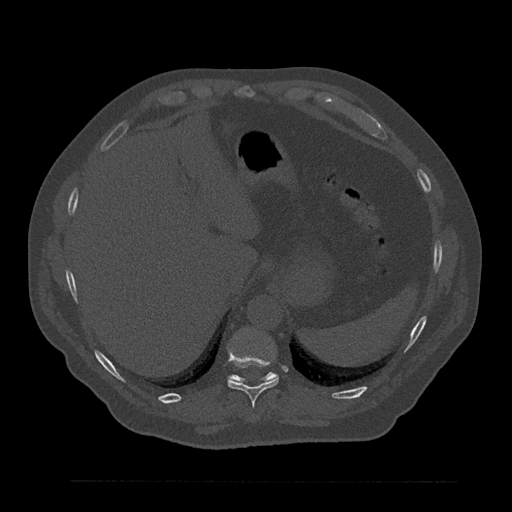
CT including the spine, one axial slice; position 333 of 797 along the scan axis; 120 kVp; bone window (W 1800 / L 400 HU); 512 × 512 image matrix, field of view 430 × 430 mm. Male patient, age 61 years. Case-level facts recorded for this patient, not image findings: primary cancer: prostate.
Outlined on this slice (semi-automatically segmented with operator editing):
- T10 vertebra: bounding box [x1, y1, x2, y2] px = [227, 347, 279, 407]
- T11 vertebra: [228, 373, 278, 382]